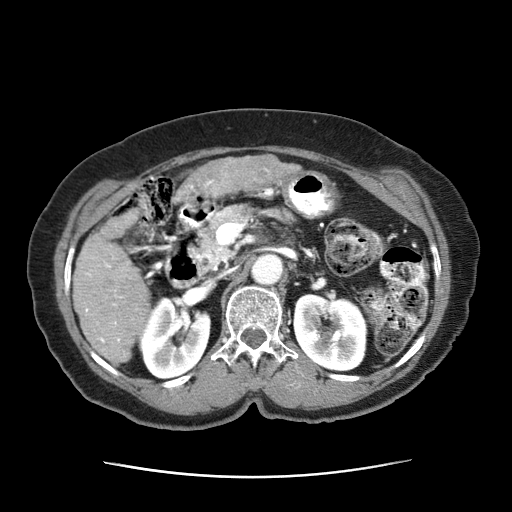
Contrast-enhanced abdominal CT (liver protocol), one axial slice. Position 20 of 63 along the scan axis. Soft-tissue window (W 400 / L 40 HU). 512 × 512 image matrix, field of view 360 × 360 mm. Female patient, age 79 years. Case-level facts recorded for this patient, not image findings: diagnosis: hepatocellular carcinoma (patient treated with transarterial chemoembolisation; whether this scan precedes or follows treatment is not stated here); TNM stage (as recorded): Stage-II; Child-Pugh class: B; tumour nodularity: multinodular.
Structures marked on this image (semi-automatic segmentation, software-assisted and operator-edited):
- abdominal aorta: box from (x=252, y=251) to (x=284, y=283) px
- liver parenchyma outside the tumour (the mass and vessels are separate outlines, so this box may not span the whole liver): (x=73, y=207)–(x=155, y=367)
- mass: (x=179, y=156)–(x=302, y=198)
- liver vessels: (x=85, y=263)–(x=130, y=343)